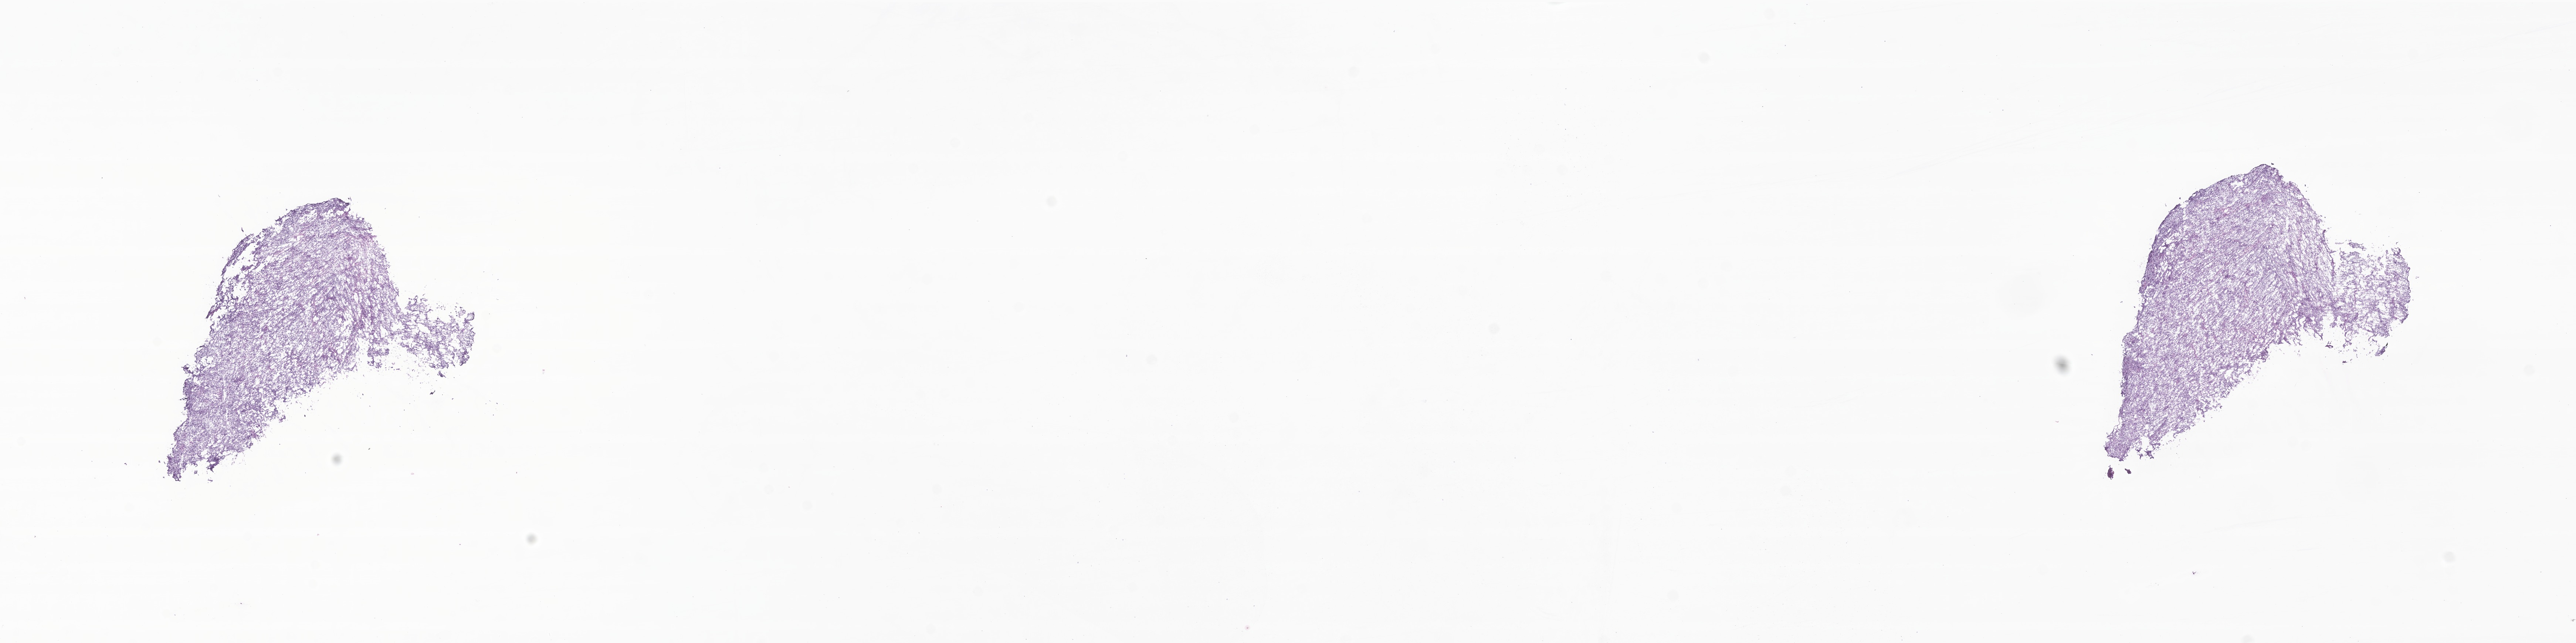
Haematoxylin and eosin whole-slide image of tumor tissue from the urachus, whole scanned area (about 29.4 x 7.3 mm) shown as a low-resolution overview; cryosection (OCT / tissue freezing medium). Patient female; age 37 months (3 years 1 month).
Recorded diagnosis: Embryonal rhabdomyosarcoma, NOS.